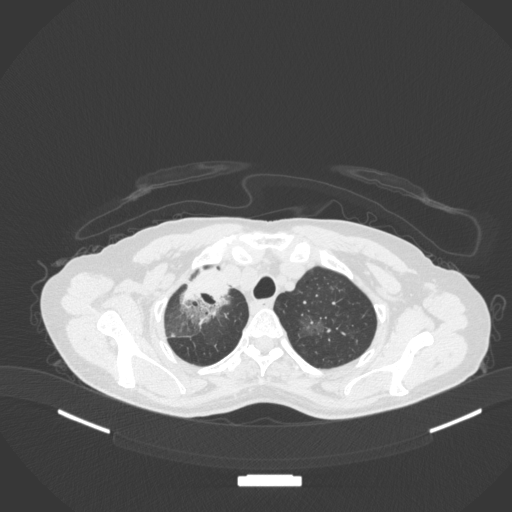
Chest CT, one axial slice. Position 276 of 311 along the scan axis. 120 kVp. Lung window (W 1500 / L -600 HU). 1 mm slice thickness. 512 × 512 image matrix, field of view 400 × 400 mm. Female patient, age 59 years. From the clinical record (not read from this slice): clinical TNM (as recorded): T3 N0 M0; histopathological grade: G1.
Annotated regions visible in this slice (rectangle marked by the reading radiologist):
- lung tumour (recorded histology: adenocarcinoma): bounding box <177,263,234,325> (left, top, right, bottom; pixels)